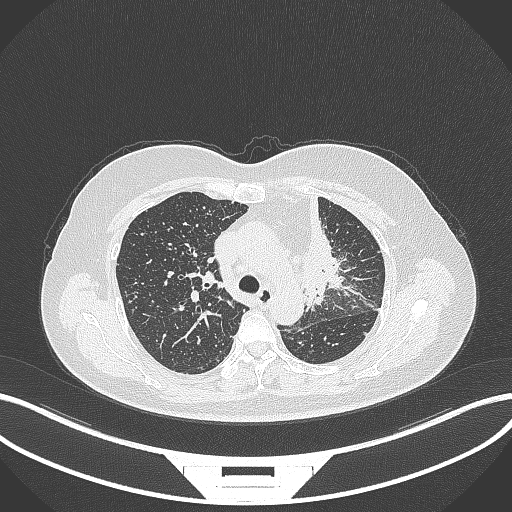
Chest CT, one axial slice; position 233 of 348 along the scan axis; reconstruction kernel B70f; 120 kVp; lung window (W 1500 / L -600 HU); 1 mm slice thickness; 512 × 512 image matrix, field of view 400 × 400 mm. Female patient, age 49 years. Case-level facts recorded for this patient, not image findings: clinical TNM (as recorded): T1c N0 M1.
Annotated regions visible in this slice (bounding box drawn by a radiologist):
- lung tumour (recorded histology: adenocarcinoma): box from (x=283, y=192) to (x=343, y=303) px